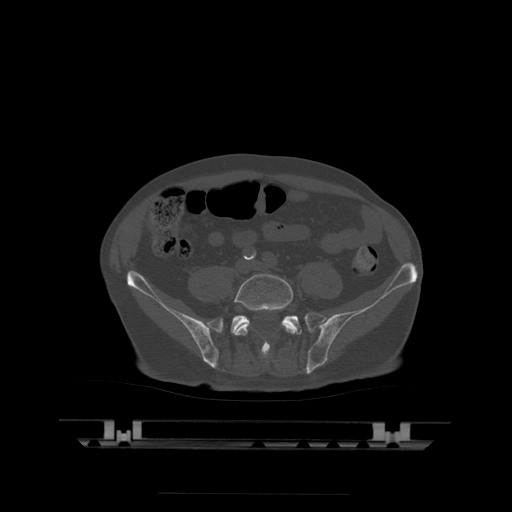
CT including the spine, one axial slice. Position 66 of 522 along the scan axis. Bone window (W 1800 / L 400 HU). 512 × 512 image matrix, field of view 436 × 436 mm. Patient age 68 years. From the clinical record (not read from this slice): primary cancer: urothelial.
Structures marked on this image (semi-automatically segmented with operator editing):
- L5 vertebra: bounding box <234,274,296,355> (left, top, right, bottom; pixels)